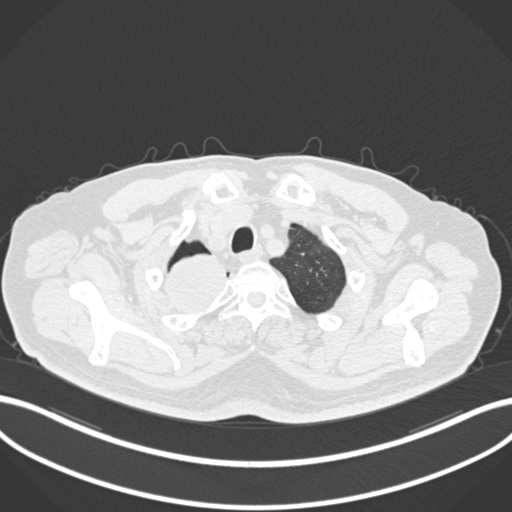
Chest CT, one axial slice; slice 192 of 218 in the series (ordered by position); reconstruction kernel B30f; 120 kVp; lung window (W 1500 / L -600 HU); 1 mm slice thickness; 512 × 512 image matrix, field of view 400 × 400 mm. Patient: male, 68 years. From the clinical record (not read from this slice): clinical TNM (as recorded): T2a N0 M0.
Annotated regions visible in this slice (bounding box drawn by a radiologist):
- lung tumour (recorded histology: adenocarcinoma): bounding box <160,248,234,324> (left, top, right, bottom; pixels)